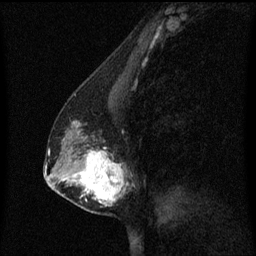
Breast MRI (dynamic contrast-enhanced), one sagittal slice. Slice 30 of 60 in the series (ordered by position). Dynamic contrast-enhanced series, image 2 of 3 at this slice position (ordered by acquisition). 1.5 T. TE 4.2 ms, TR 8.4 ms. 2 mm slice thickness. 256 × 256 image matrix. Patient: female, 40 years. Case-level facts recorded for this patient, not image findings: setting: breast cancer imaged before/during neoadjuvant chemotherapy; receptor status: triple-negative.
Structures marked on this image (semi-automatic segmentation, software-assisted and operator-edited):
- analysis volume of interest (the breast-tissue region the enhancement analysis was run in; not a lesion): box from (x=60, y=120) to (x=133, y=215) px
- tumour enhancement mask (voxels above the 70 % enhancement threshold inside the analysis volume of interest): (x=62, y=150)–(x=125, y=205)